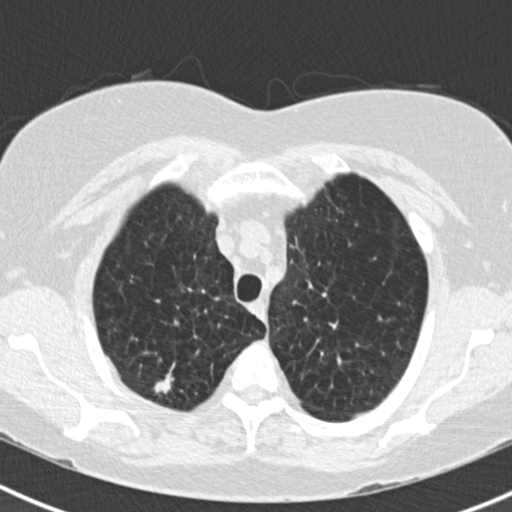
Low-dose screening chest CT, one axial slice; position 142 of 180 along the scan axis; 120 kVp; lung window (W 1500 / L -600 HU); 512 × 512 image matrix, field of view 310 × 310 mm.
Structures marked on this image (outlined manually by an expert reader):
- lesion 1 (tumor, upper lobe of right lung): bounding box (x1, y1, x2, y2) in pixels: (154, 373, 174, 394)